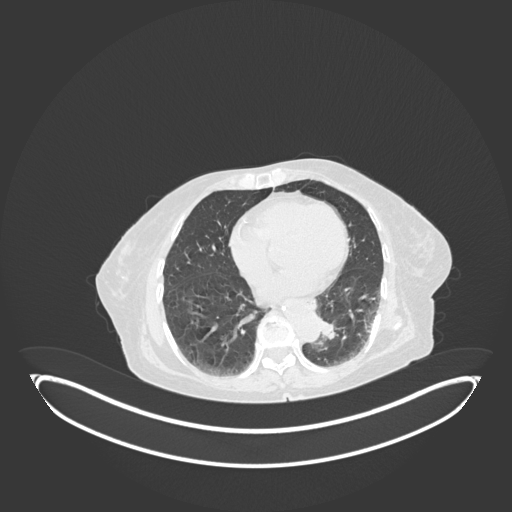
Chest CT, one axial slice; position 31 of 189 along the scan axis; reconstruction kernel B30f; lung window (W 1500 / L -600 HU); 1 mm slice thickness; 512 × 512 image matrix, field of view 500 × 500 mm. Patient: female, 82 years. From the clinical record (not read from this slice): clinical TNM (as recorded): T1b N0 M1.
Annotated regions visible in this slice (bounding box drawn by a radiologist):
- lung tumour (recorded histology: adenocarcinoma): bounding box [x1, y1, x2, y2] px = [320, 317, 339, 345]